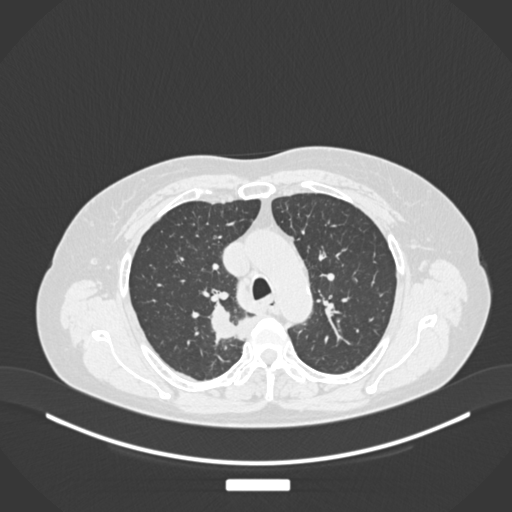
Chest CT, one axial slice; slice 185 of 237 in the series (ordered by position); lung window (W 1500 / L -600 HU); 512 × 512 image matrix, field of view 400 × 400 mm. Female patient, age 62 years. From the clinical record (not read from this slice): clinical TNM (as recorded): T1c N1 M0.
Outlined on this slice (bounding box drawn by a radiologist):
- lung tumour (recorded histology: squamous cell carcinoma): bounding box <207,301,250,357> (left, top, right, bottom; pixels)